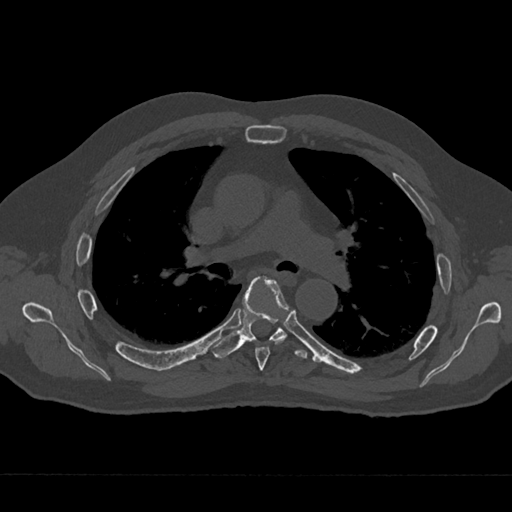
CT including the spine, one axial slice. Position 448 of 797 along the scan axis. Reconstruction kernel Br40s/3. Bone window (W 1800 / L 400 HU). 512 × 512 image matrix, field of view 377 × 377 mm. Male patient, age 75 years. From the clinical record (not read from this slice): primary cancer: renal; vertebrae with lytic lesions (as recorded): T4.
Outlined on this slice (semi-automatically segmented with operator editing):
- T5 vertebra: bounding box [x1, y1, x2, y2] px = [255, 280, 290, 371]
- T6 vertebra: [210, 276, 308, 359]